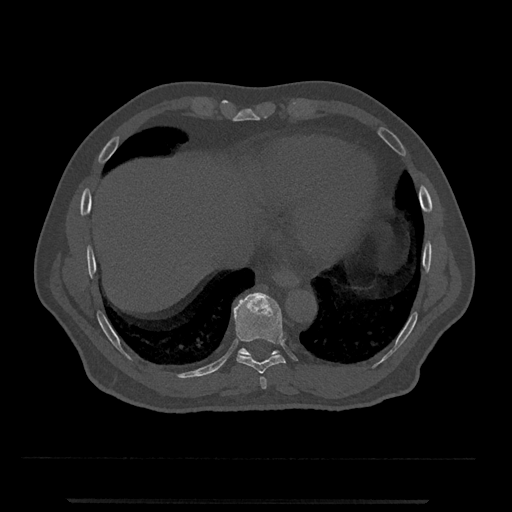
CT including the spine, one axial slice. Position 561 of 797 along the scan axis. 120 kVp. Bone window (W 1800 / L 400 HU). 0.5 mm slice thickness. 512 × 512 image matrix, field of view 419 × 419 mm. Male patient, age 63 years. Case-level facts recorded for this patient, not image findings: primary cancer: prostate.
Outlined on this slice (semi-automatically segmented with operator editing):
- T10 vertebra: bounding box [x1, y1, x2, y2] px = [238, 348, 280, 358]
- T8 vertebra: [260, 377, 267, 389]
- T9 vertebra: [233, 292, 286, 374]